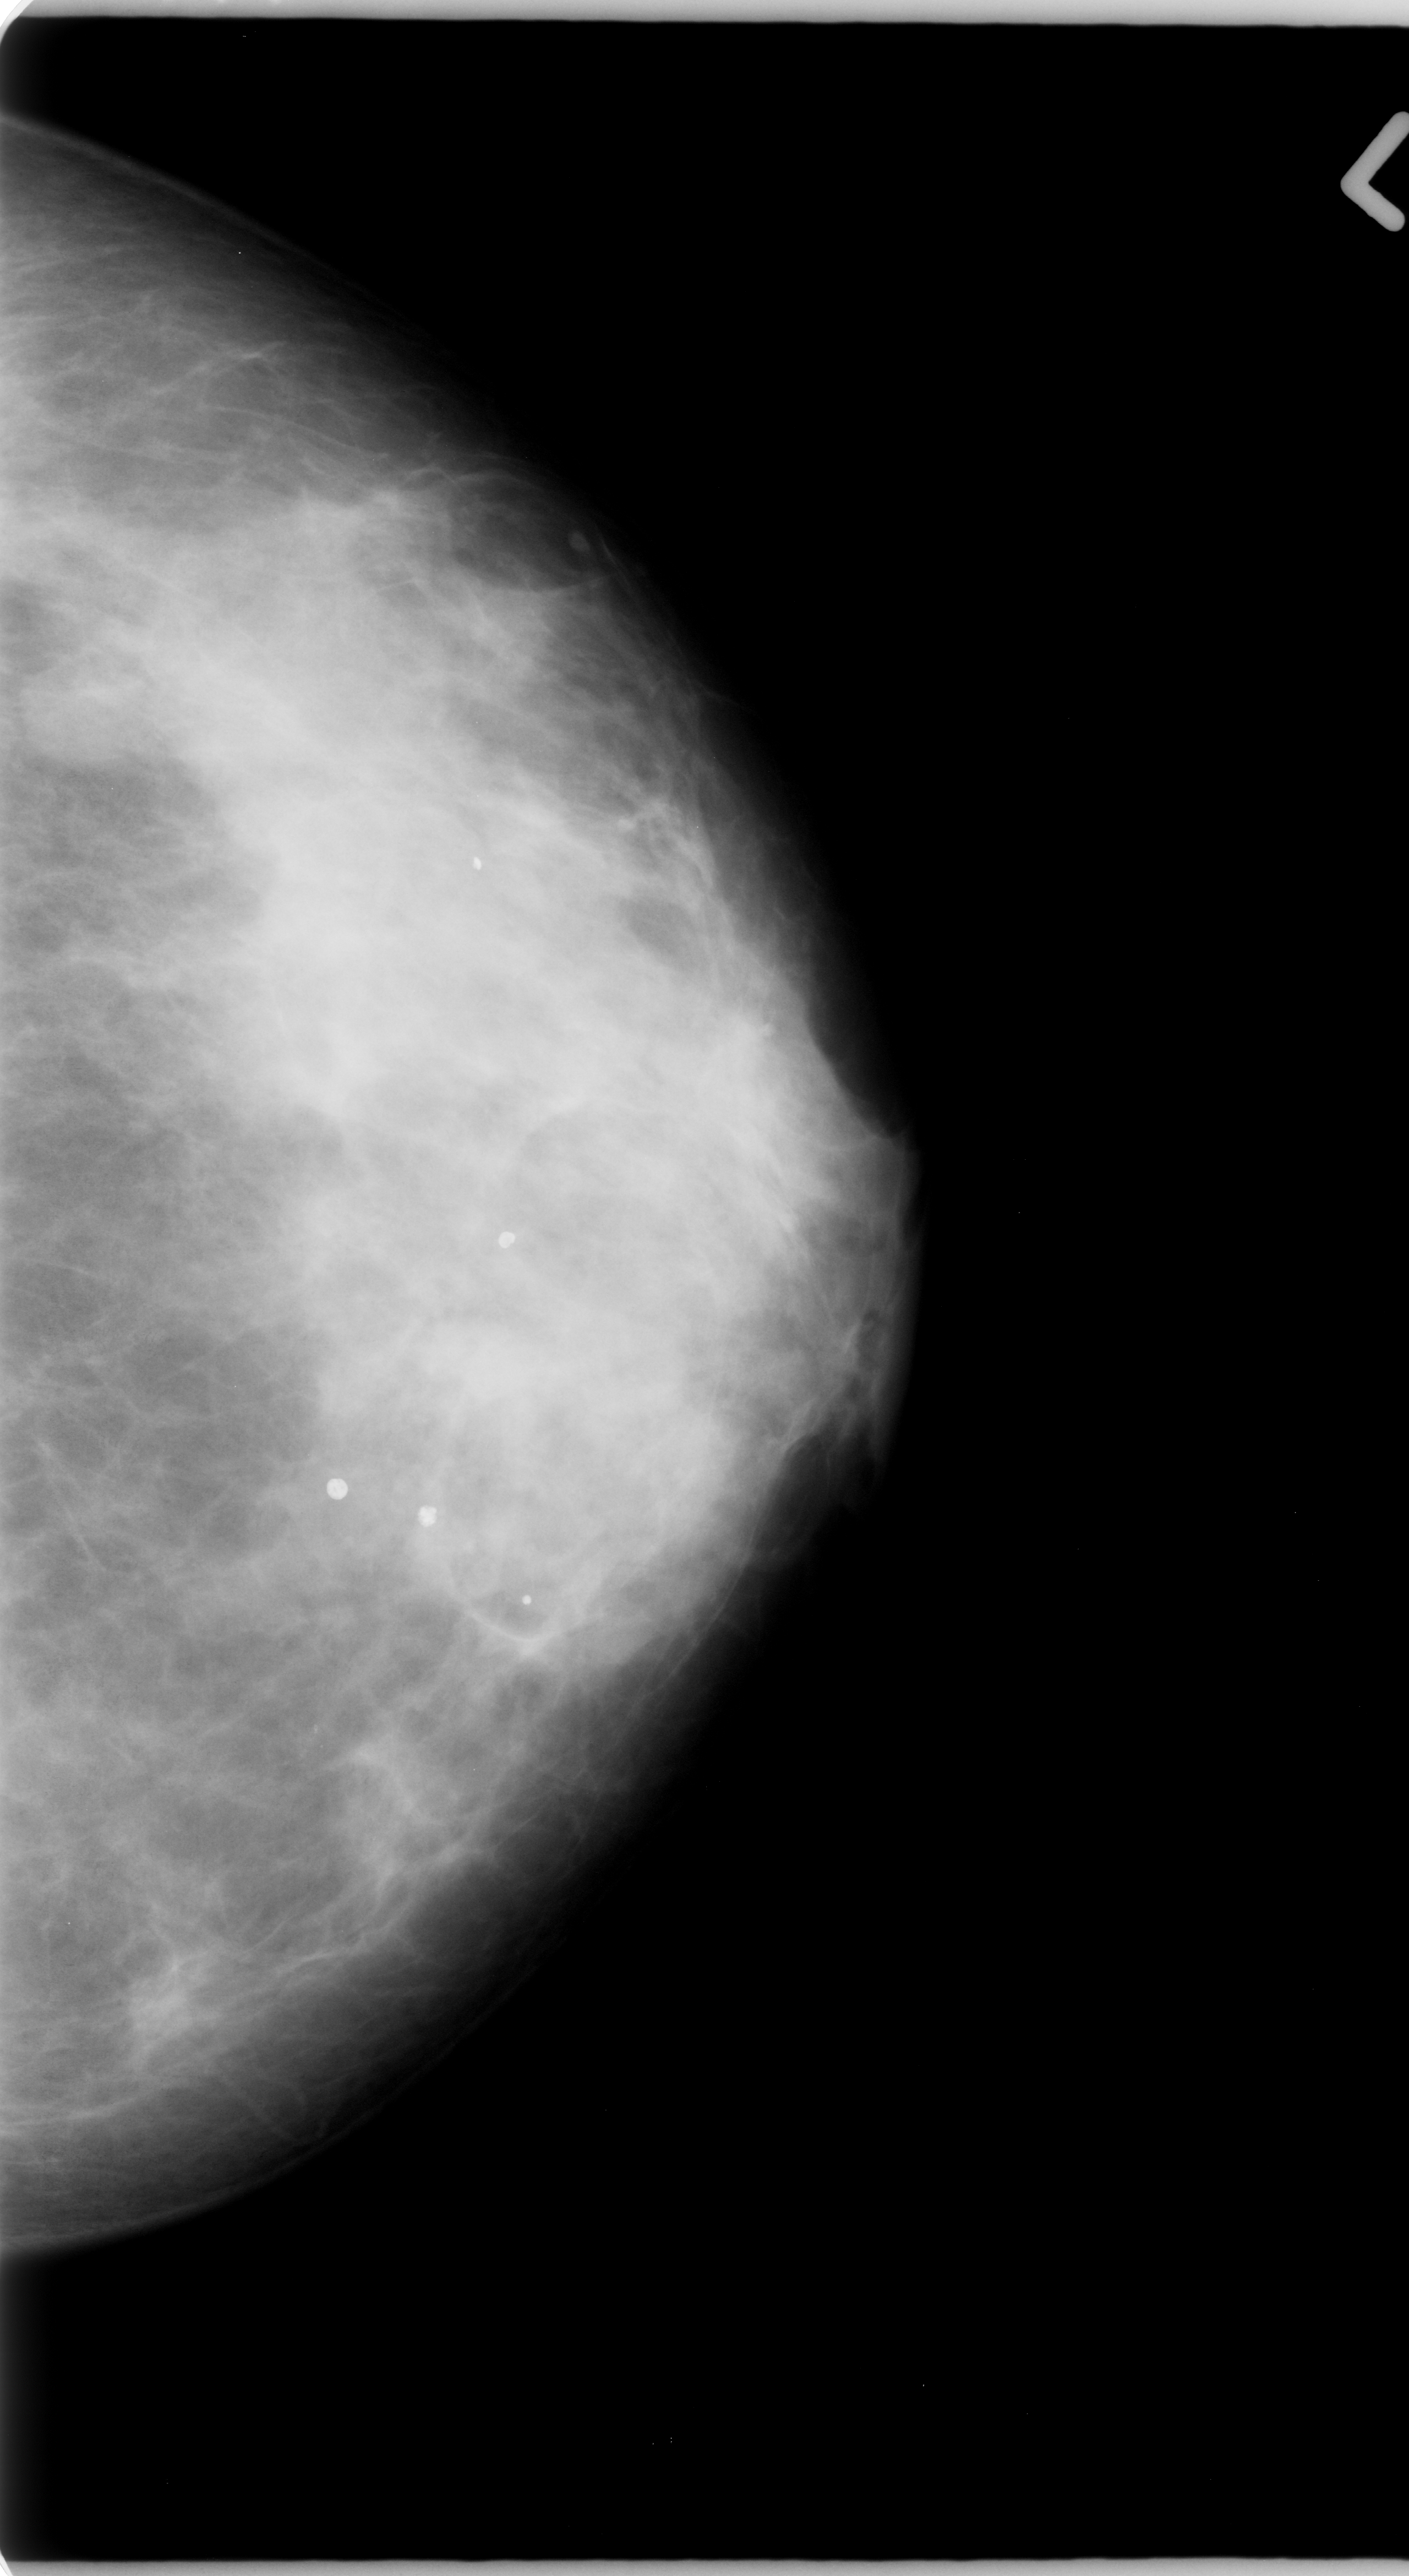
Scanned film-screen mammogram. Left breast. CC view. Breast composition: heterogeneously dense (BI-RADS density category 3 of 4). 1409 × 2576 image matrix.
Expert-marked regions of interest on this image (one box per marked abnormality):
- mass, shape oval, margins microlobulated; BI-RADS assessment category 4; subtlety rating 4 on a 1 (subtle) to 5 (obvious) scale; pathology (as recorded): malignant: bounding box [x1, y1, x2, y2] px = [28, 614, 166, 774]